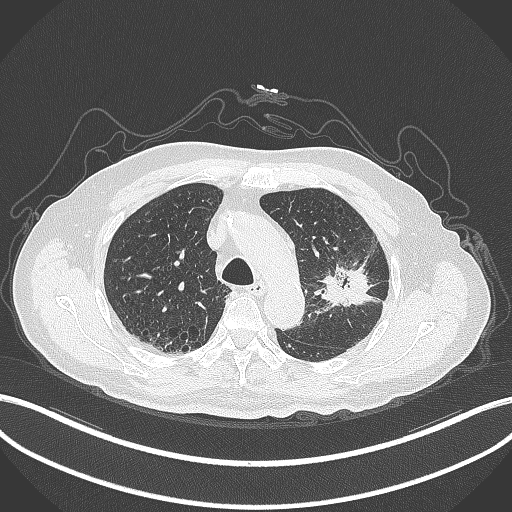
Chest CT, one axial slice. Position 216 of 331 along the scan axis. Lung window (W 1500 / L -600 HU). 512 × 512 image matrix. Male patient, age 79 years. Case-level facts recorded for this patient, not image findings: clinical TNM (as recorded): T2a N1 M1; histopathological grade: G3.
Annotated regions visible in this slice (rectangle marked by the reading radiologist):
- lung tumour (recorded histology: adenocarcinoma): bounding box <315,246,382,312> (left, top, right, bottom; pixels)